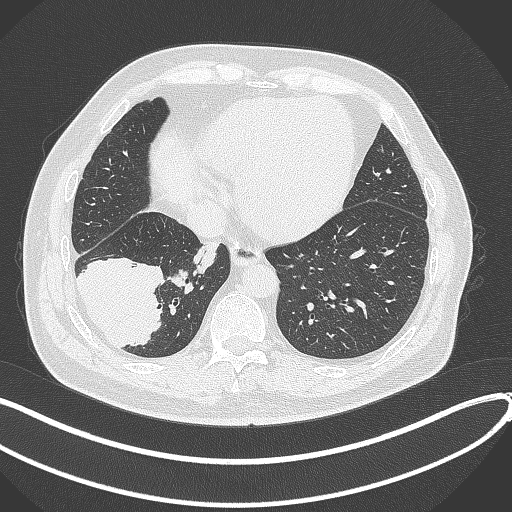
Chest CT, one axial slice. Slice 100 of 360 in the series (ordered by position). Reconstruction kernel B70f. 120 kVp. Lung window (W 1500 / L -600 HU). 1 mm slice thickness. 512 × 512 image matrix. Patient: male, 59 years.
Outlined on this slice (rectangle marked by the reading radiologist):
- lung tumour (recorded histology: adenocarcinoma): bounding box (x1, y1, x2, y2) in pixels: (73, 250, 169, 353)